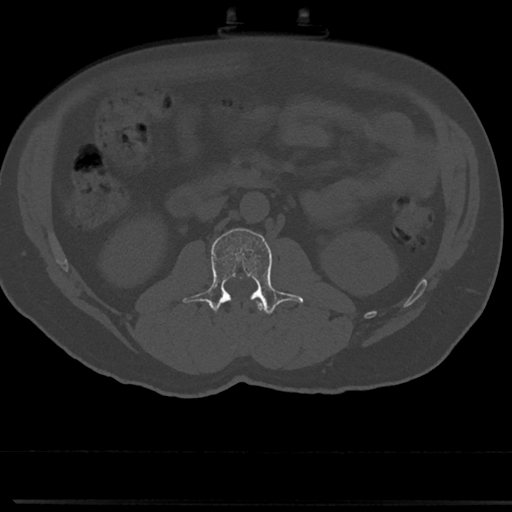
CT including the spine, one axial slice; reconstruction kernel Br40s/3; 120 kVp; bone window (W 1800 / L 400 HU); 0.5 mm slice thickness; 512 × 512 image matrix, field of view 355 × 355 mm. Male patient, age 61 years. Case-level facts recorded for this patient, not image findings: primary cancer: prostate.
Outlined on this slice (semi-automatically segmented with operator editing):
- L1 vertebra: bounding box <239,299,263,344> (left, top, right, bottom; pixels)
- L2 vertebra: <191,228,303,315>